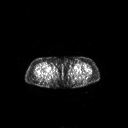
FDG PET of an extremity soft-tissue mass (from a PET/CT study), one axial slice. Slice 247 of 311 in the series (ordered by position). 3.27 mm slice thickness. 128 × 128 image matrix, field of view 700 × 700 mm. Patient: female, 78 years. Case-level facts recorded for this patient, not image findings: histological type: leiomyosarcoma; grade: intermediate; site of the primary tumour: parascapusular.
Outlined on this slice (expert contour drawn on MRI and transferred to this co-registered scan by the dataset authors):
- gross tumour volume including surrounding oedema: bounding box [x1, y1, x2, y2] px = [54, 66, 56, 68]
- gross tumour volume (mass): [54, 66, 56, 68]